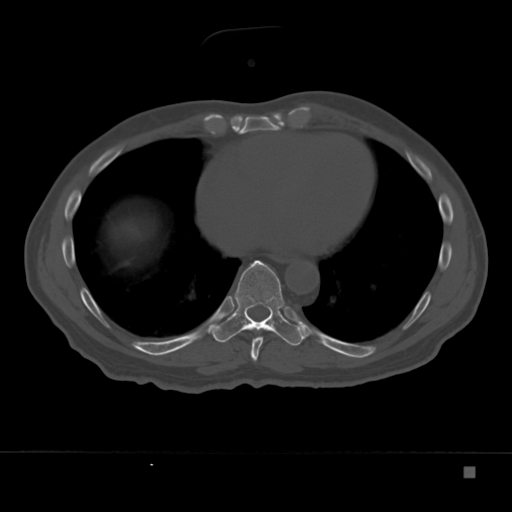
CT including the spine, one axial slice; position 194 of 332 along the scan axis; reconstruction kernel Br40s; bone window (W 1800 / L 400 HU); 512 × 512 image matrix, field of view 389 × 389 mm. Male patient, age 72 years. From the clinical record (not read from this slice): primary cancer: skeletal.
Structures marked on this image (semi-automatic segmentation, software-assisted and operator-edited):
- T8 vertebra: bounding box [x1, y1, x2, y2] px = [250, 336, 263, 362]
- T9 vertebra: [213, 260, 304, 346]